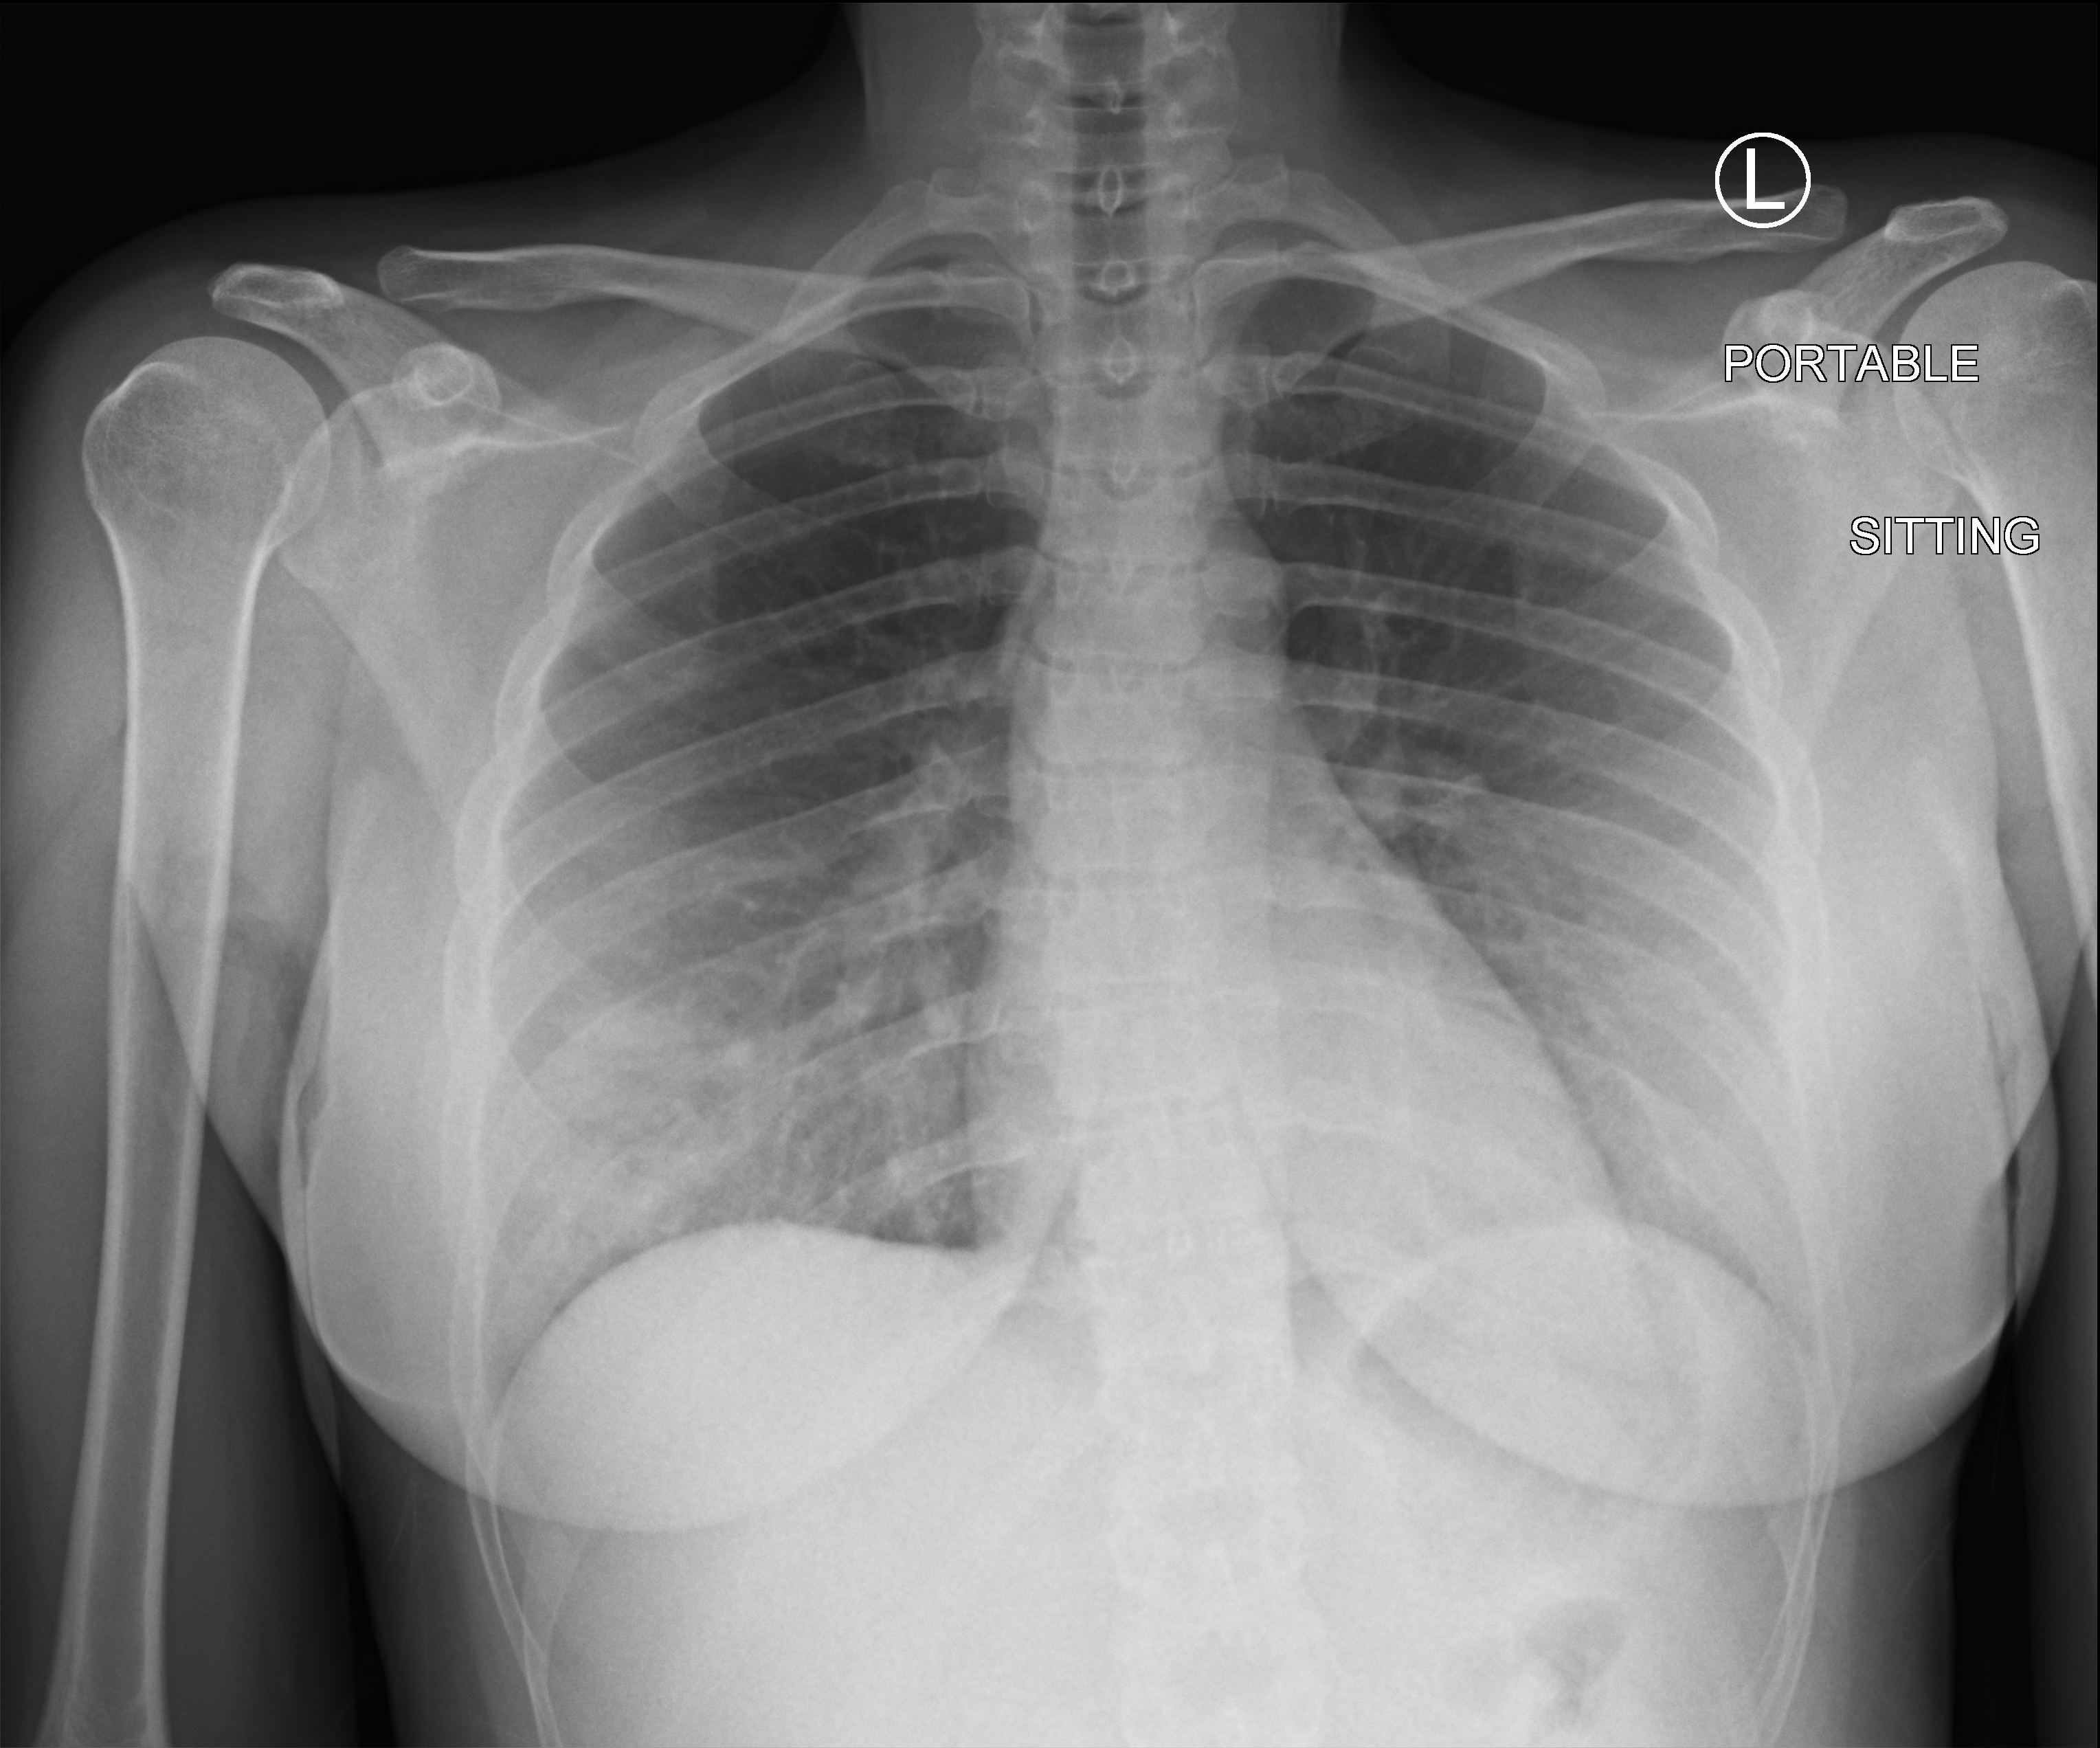
Chest X-ray (portable), anteroposterior (AP) projection. Patient hospitalised with COVID-19; female, aged 18–59 years.
Admission-level facts for this patient (not findings on this image; timing relative to this image not recorded): mechanically ventilated during this hospital stay: no.